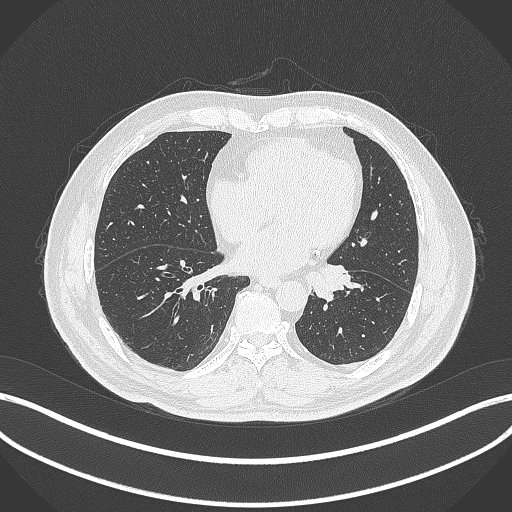
Chest CT, one axial slice; slice 104 of 312 in the series (ordered by position); reconstruction kernel B70f; 120 kVp; lung window (W 1500 / L -600 HU); 1 mm slice thickness; 512 × 512 image matrix, field of view 400 × 400 mm. Male patient, age 71 years. From the clinical record (not read from this slice): clinical TNM (as recorded): T1b N0 M0.
Structures marked on this image (rectangle marked by the reading radiologist):
- lung tumour (recorded histology: squamous cell carcinoma): box from (x=304, y=262) to (x=358, y=301) px